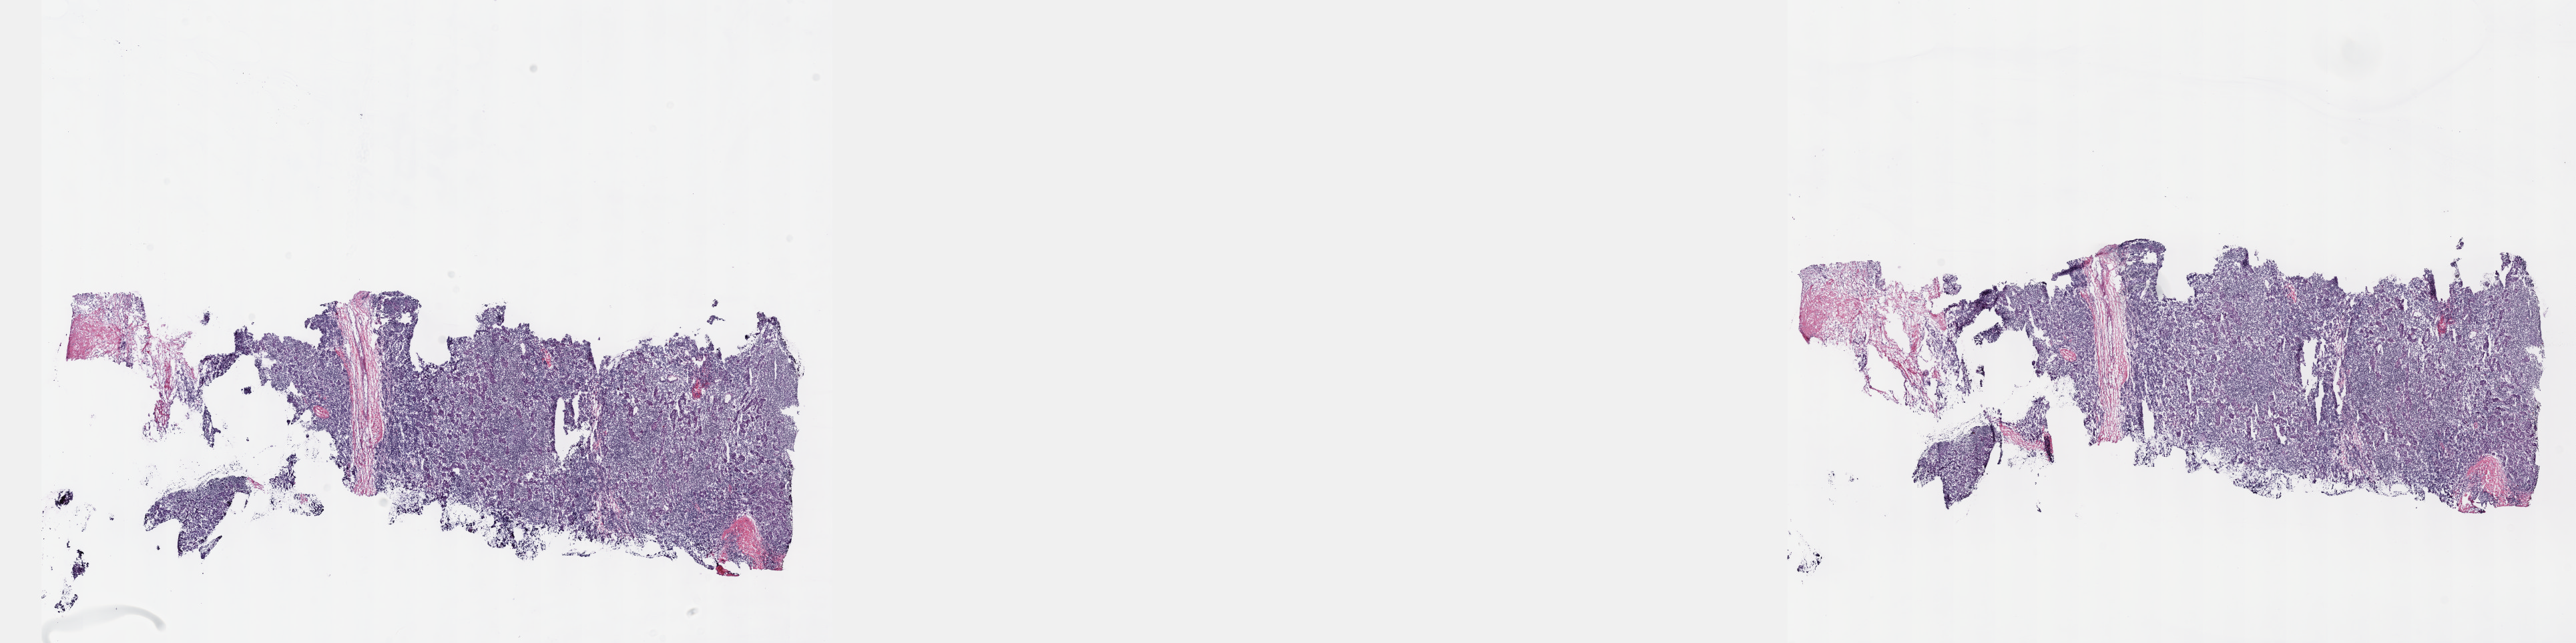
Whole-slide histology image, Hematoxylin and eosin (H&E) stained, whole scanned area (about 31.2 x 7.8 mm) shown as a low-resolution overview; frozen section from the top of the tissue portion; thymus, primary tumour sample. Female patient; age at initial diagnosis 71 years. Pathologist review of this section (percent, as recorded): tumour cells 90%, tumour nuclei 95%, normal cells 0%, stromal cells 10%, necrosis 0%. Infiltration values recorded for this section: lymphocyte infiltration 0%, monocyte infiltration 0%, neutrophil infiltration 0%.
Diagnosis: Thymoma, type A, malignant.